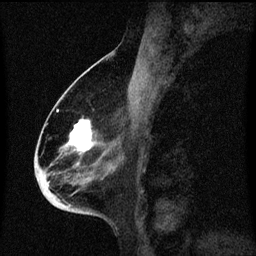
Breast MRI (dynamic contrast-enhanced), one sagittal slice. Slice 33 of 60 in the series (ordered by position). Dynamic contrast-enhanced series, image 2 of 3 at this slice position (ordered by acquisition). 1.5 T. TE 4.2 ms, TR 8.4 ms. 2 mm slice thickness. 256 × 256 image matrix, field of view 200 × 200 mm. Patient: female, 68 years. Case-level facts recorded for this patient, not image findings: setting: breast cancer imaged before/during neoadjuvant chemotherapy; receptor status: triple-negative.
Outlined on this slice (semi-automatic segmentation, software-assisted and operator-edited):
- analysis volume of interest (the breast-tissue region the enhancement analysis was run in; not a lesion): bounding box (x1, y1, x2, y2) in pixels: (37, 96, 113, 213)
- tumour enhancement mask (voxels above the 70 % enhancement threshold inside the analysis volume of interest): (41, 120, 93, 187)